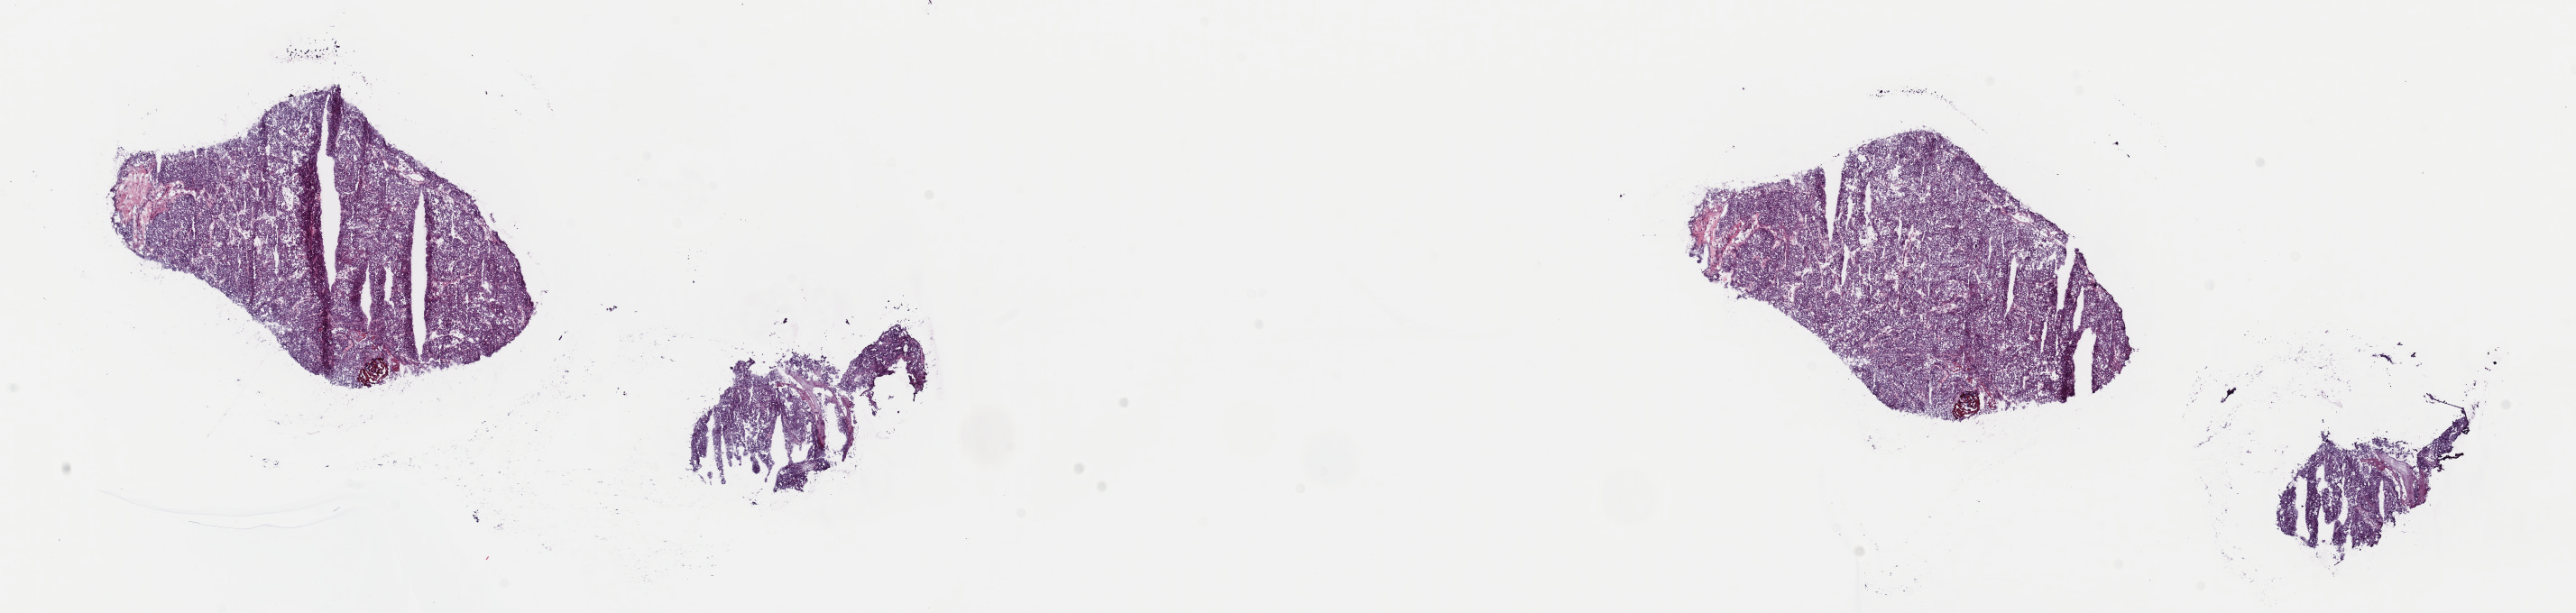
Hematoxylin and eosin (H&E) stained whole-slide image — low-resolution overview of the scanned area, about 22.6 x 5.4 mm. Frozen section from the top of the tissue portion. Primary tumour sample from the kidney. Female, age 62 years at initial diagnosis. Histologic grade: G3 (poorly differentiated). Composition of this section per pathologist review: tumour cells 100%, tumour nuclei 95%, normal cells 0%, stromal cells 0%, necrosis 0%. Infiltration values recorded for this section: lymphocyte infiltration 0%, monocyte infiltration 0%, neutrophil infiltration 0%.
- AJCC pathologic stage: I
- pathologic diagnosis: Renal cell carcinoma, NOS
- laterality: right